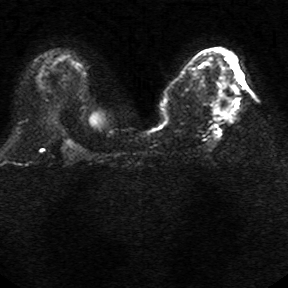
Breast MRI, one axial slice. Position 15 of 34 along the scan axis. Diffusion-weighted series; image 2 of 4 stored at this slice position (different b-values; order by instance number). 1.5 T. 288 × 288 image matrix, field of view 340 × 340 mm. Female patient.
Structures marked on this image (outlined manually by an expert reader):
- tumour on diffusion-weighted imaging: bounding box [x1, y1, x2, y2] px = [217, 81, 237, 121]